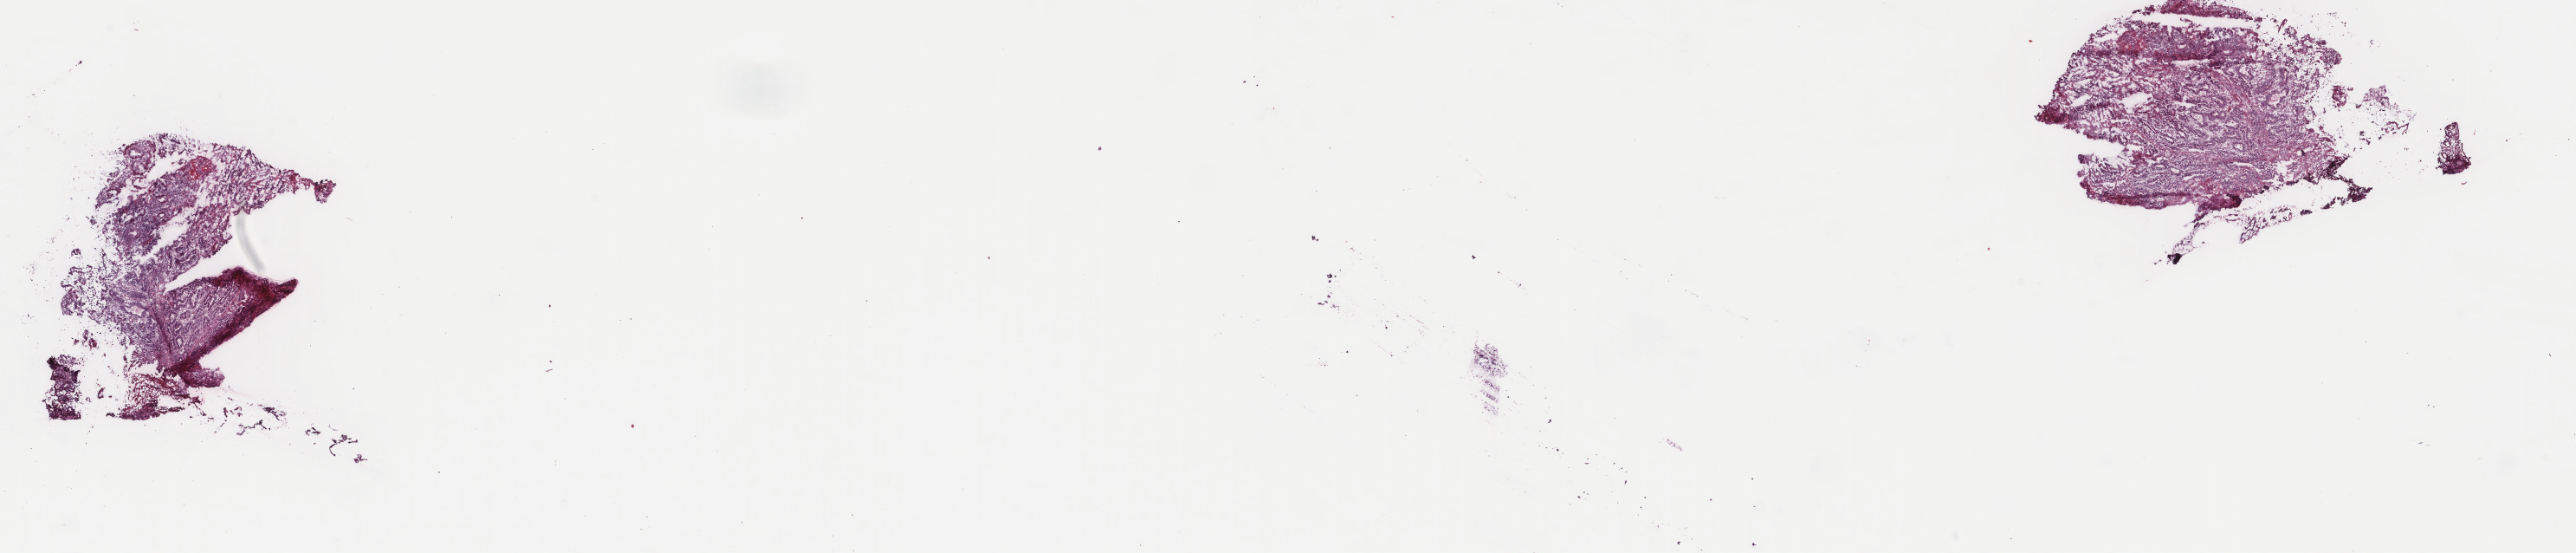
Digitized H&E-stained tissue section (whole slide), whole scanned area (about 23.6 x 5.1 mm, acquisition: 40x scan) shown as a low-resolution overview. Frozen section. Sample: primary tumour, colon. Male patient; age at initial diagnosis 76 years. Slide review estimates, as recorded: tumour cells 90%, tumour nuclei 85%, normal cells 0%, stromal cells 8%, necrosis 2%. Inflammatory infiltration, as recorded: lymphocyte infiltration 5%, monocyte infiltration 3%, neutrophil infiltration 2%.
* lymph nodes positive (case pathology): 0 of 32 examined
* AJCC pathologic stage: IIA (6th edition)
* diagnosis: Adenocarcinoma, NOS (sigmoid colon)